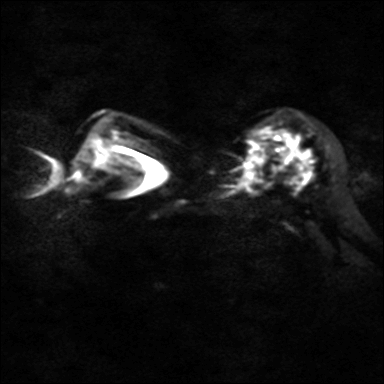
Breast MRI, one axial slice; position 26 of 40 along the scan axis; diffusion-weighted series; image 2 of 4 stored at this slice position (different b-values; order by instance number); 3 T; 4 mm slice thickness; 384 × 384 image matrix. Female patient.
Outlined on this slice (manually delineated by an expert):
- tumour on diffusion-weighted imaging: bounding box (x1, y1, x2, y2) in pixels: (248, 132, 295, 179)